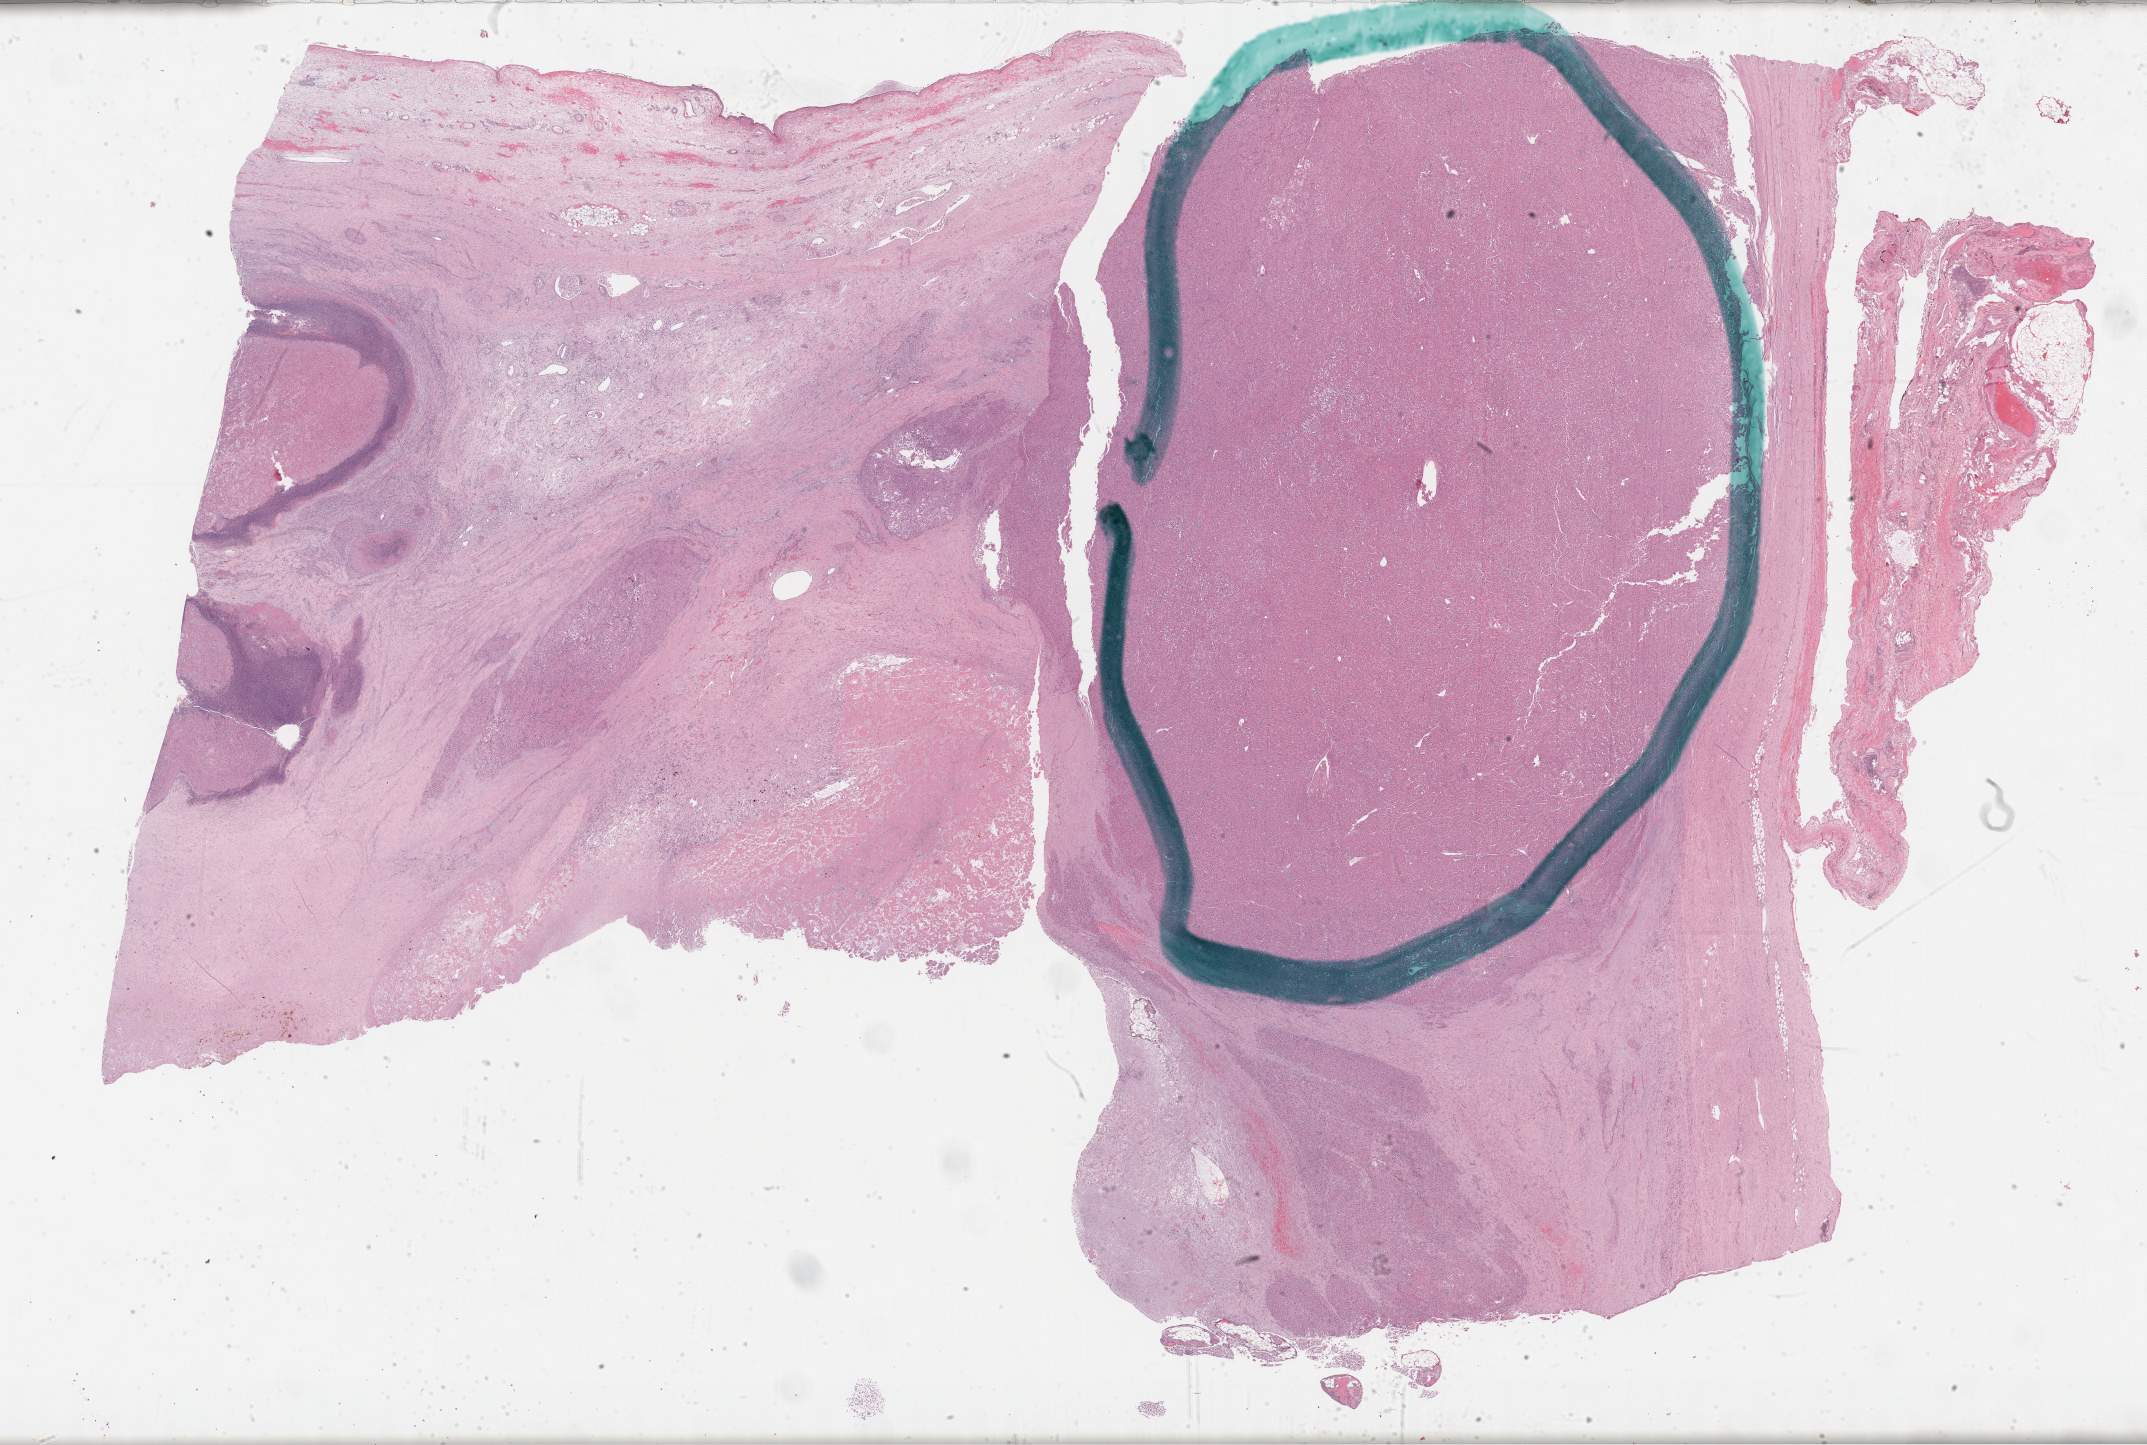
Whole-slide histology image, H&E-stained — a low-resolution overview of the entire scanned area, about 34.7 x 23.4 mm (acquisition: 40x scan), formalin-fixed paraffin-embedded (FFPE) diagnostic section, primary tumour sample from the adrenal cortex. Patient: male, age at initial diagnosis 55 years.
Histologic diagnosis: Adrenal cortical carcinoma (cortex of adrenal gland). Lymph nodes positive (case pathology): 0 of 1 examined.